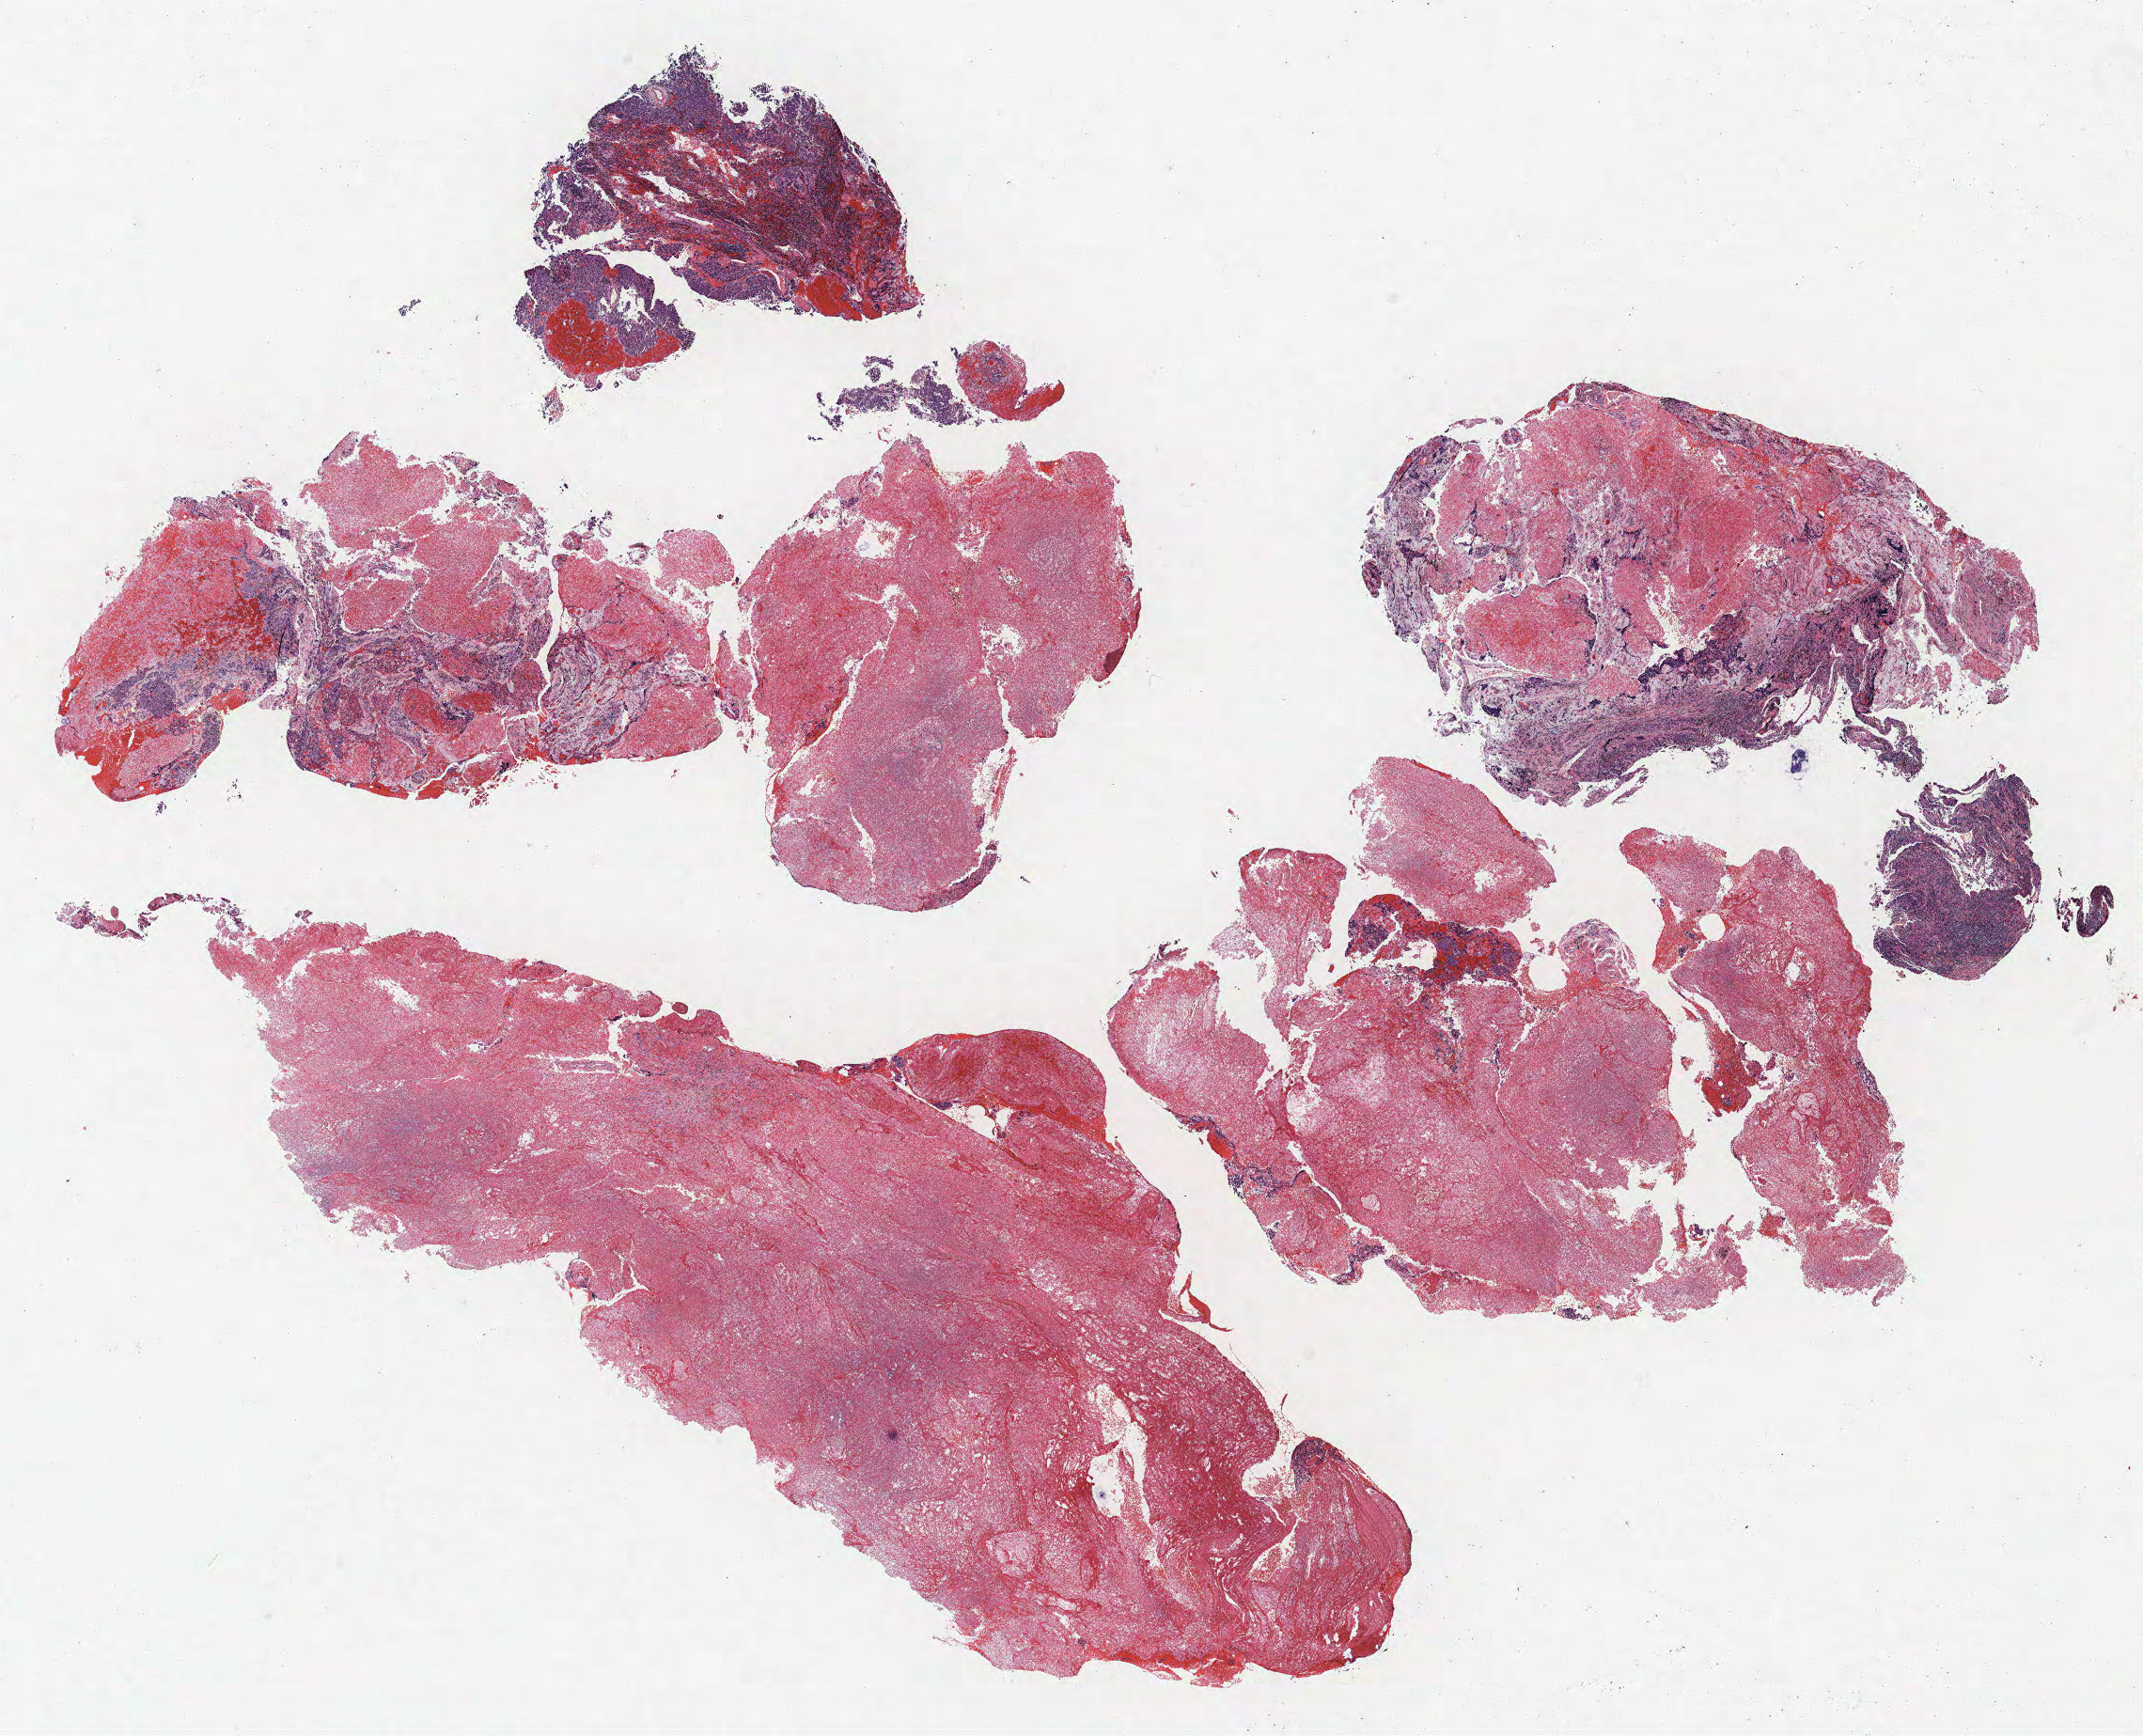
Hematoxylin and eosin (H&E) stained whole-slide image — shown as a low-resolution overview of the whole scanned area (about 18.2 x 14.8 mm, acquisition: 40x scan); FFPE section; lung tissue. Male patient, aged 62 at enrolment. Grade: poorly differentiated (G3).
• participant's lung-cancer diagnosis: Squamous cell carcinoma, NOS
• ICD-O-3 topography: lung, NOS (C34.9)
• stage (AJCC 6th edition): IV